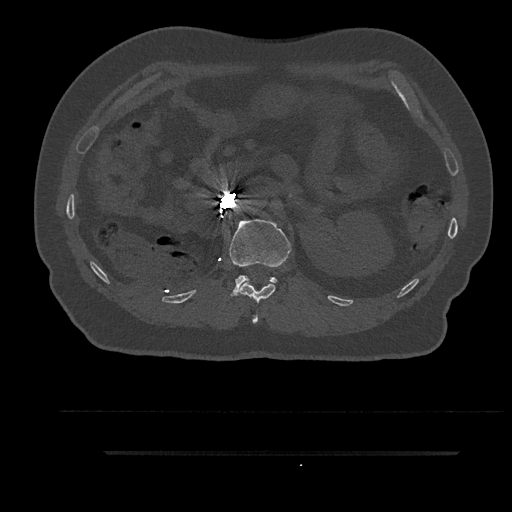
CT including the spine, one axial slice. Position 203 of 797 along the scan axis. 120 kVp. Bone window (W 1800 / L 400 HU). 0.5 mm slice thickness. 512 × 512 image matrix, field of view 432 × 432 mm. Male patient, age 63 years. From the clinical record (not read from this slice): primary cancer: renal; vertebrae with lytic lesions (as recorded): T8.
Structures marked on this image (semi-automatically segmented with operator editing):
- L1 vertebra: box from (x=229, y=219) to (x=292, y=296) px
- T12 vertebra: (x=239, y=281)–(x=276, y=324)